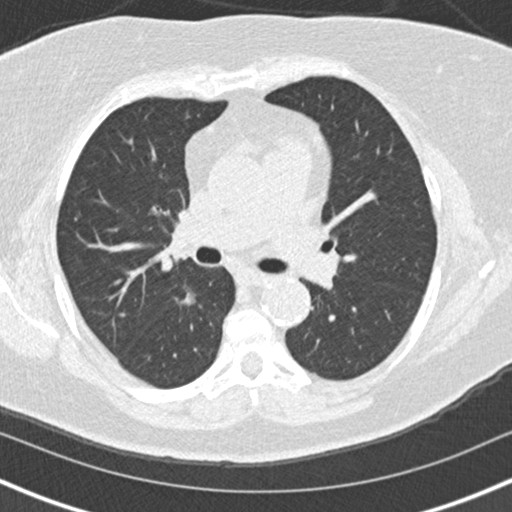
Low-dose screening chest CT, one axial slice; position 94 of 152 along the scan axis; reconstruction kernel B30f; lung window (W 1500 / L -600 HU); 512 × 512 image matrix, field of view 320 × 320 mm.
Outlined on this slice (manually delineated by an expert):
- lesion 1 (tumor, lower lobe of right lung): bounding box (x1, y1, x2, y2) in pixels: (180, 292, 195, 306)